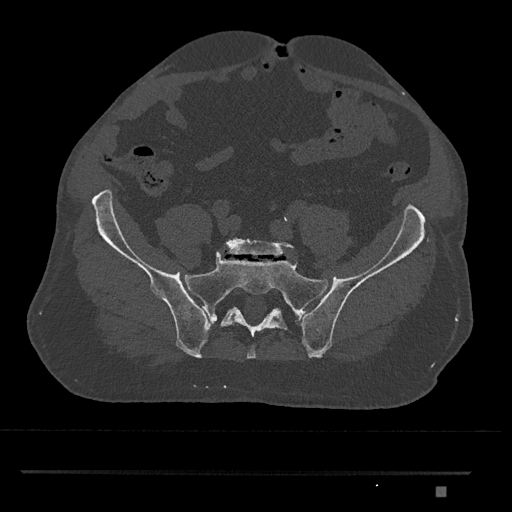
CT including the spine, one axial slice. Position 502 of 1134 along the scan axis. Reconstruction kernel Br40s/3. 120 kVp. Bone window (W 1800 / L 400 HU). 0.5 mm slice thickness. 512 × 512 image matrix, field of view 429 × 429 mm. Patient: male, 65 years. From the clinical record (not read from this slice): primary cancer: prostate.
Annotated regions visible in this slice (semi-automatically segmented with operator editing):
- L5 vertebra: bounding box [x1, y1, x2, y2] px = [224, 238, 295, 258]